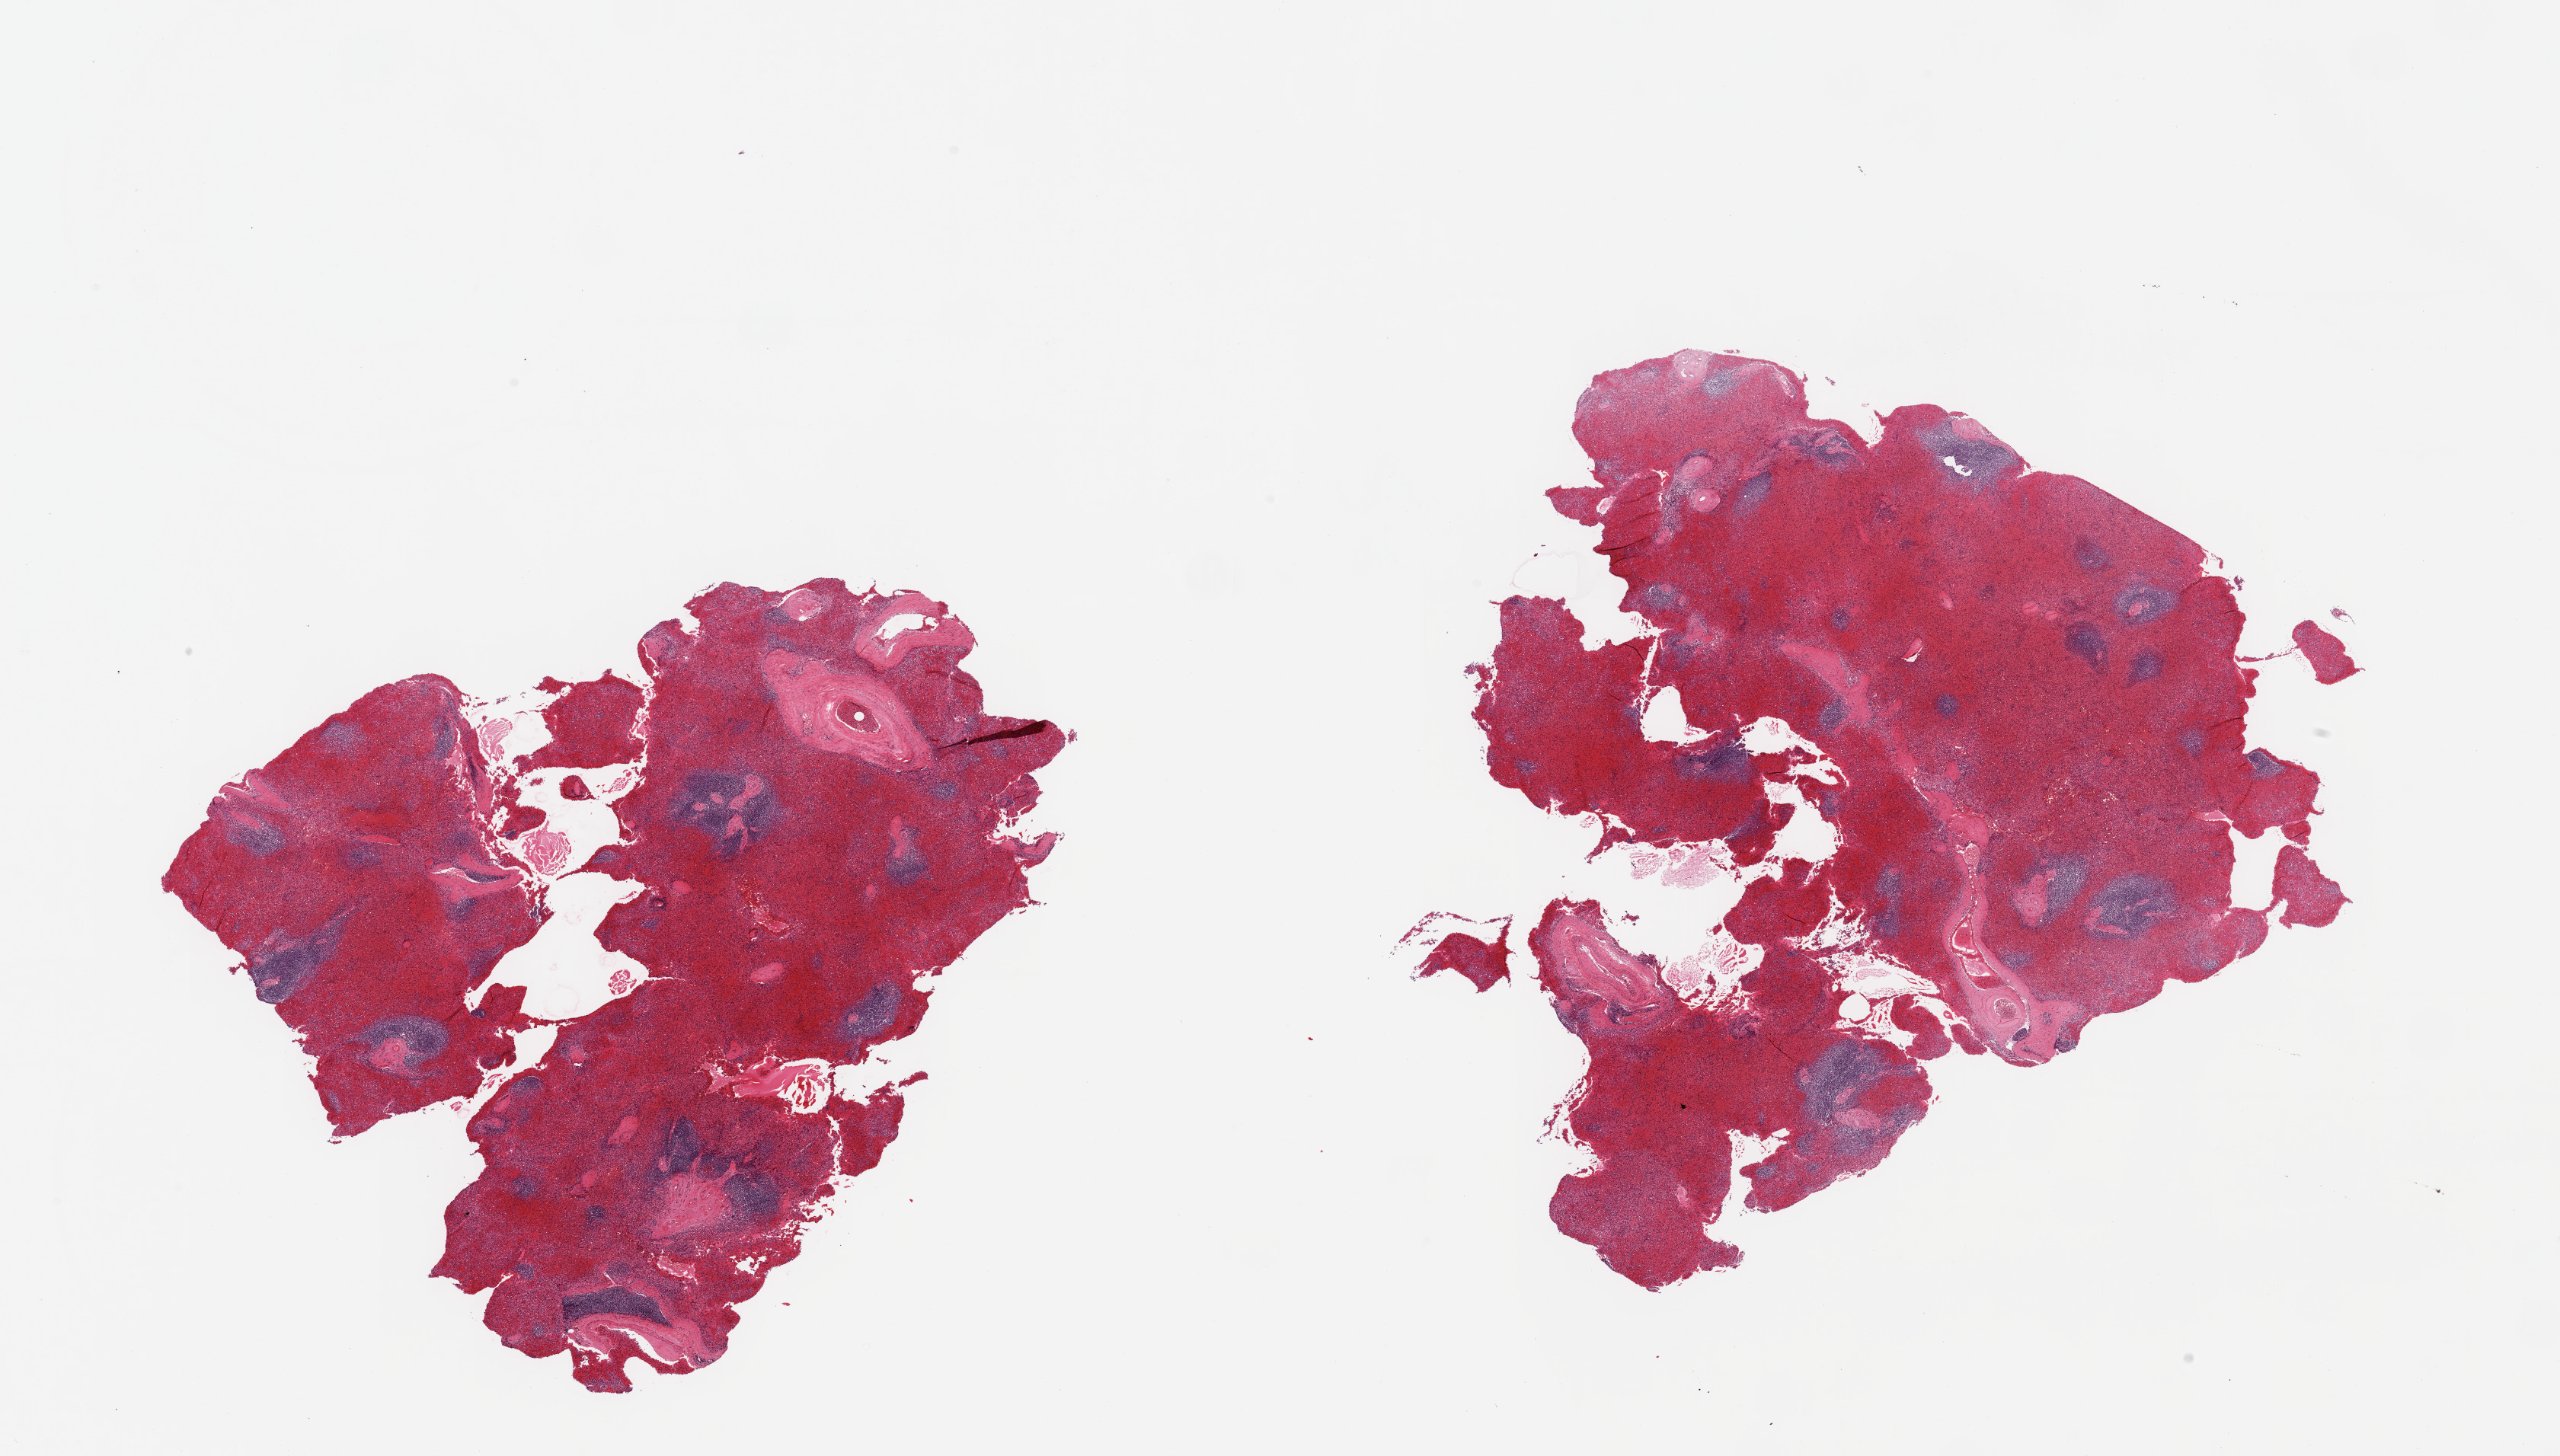
Digitized hematoxylin and eosin (H&E)-stained section, low-resolution overview of the scanned area, about 26.6 x 15.1 mm, PAXgene-fixed, paraffin-embedded tissue, sampled site (target tissue): spleen, donor tissue sample. Donor sex: male.
Review note (as recorded): 2 pieces, moderate/marked congestion.